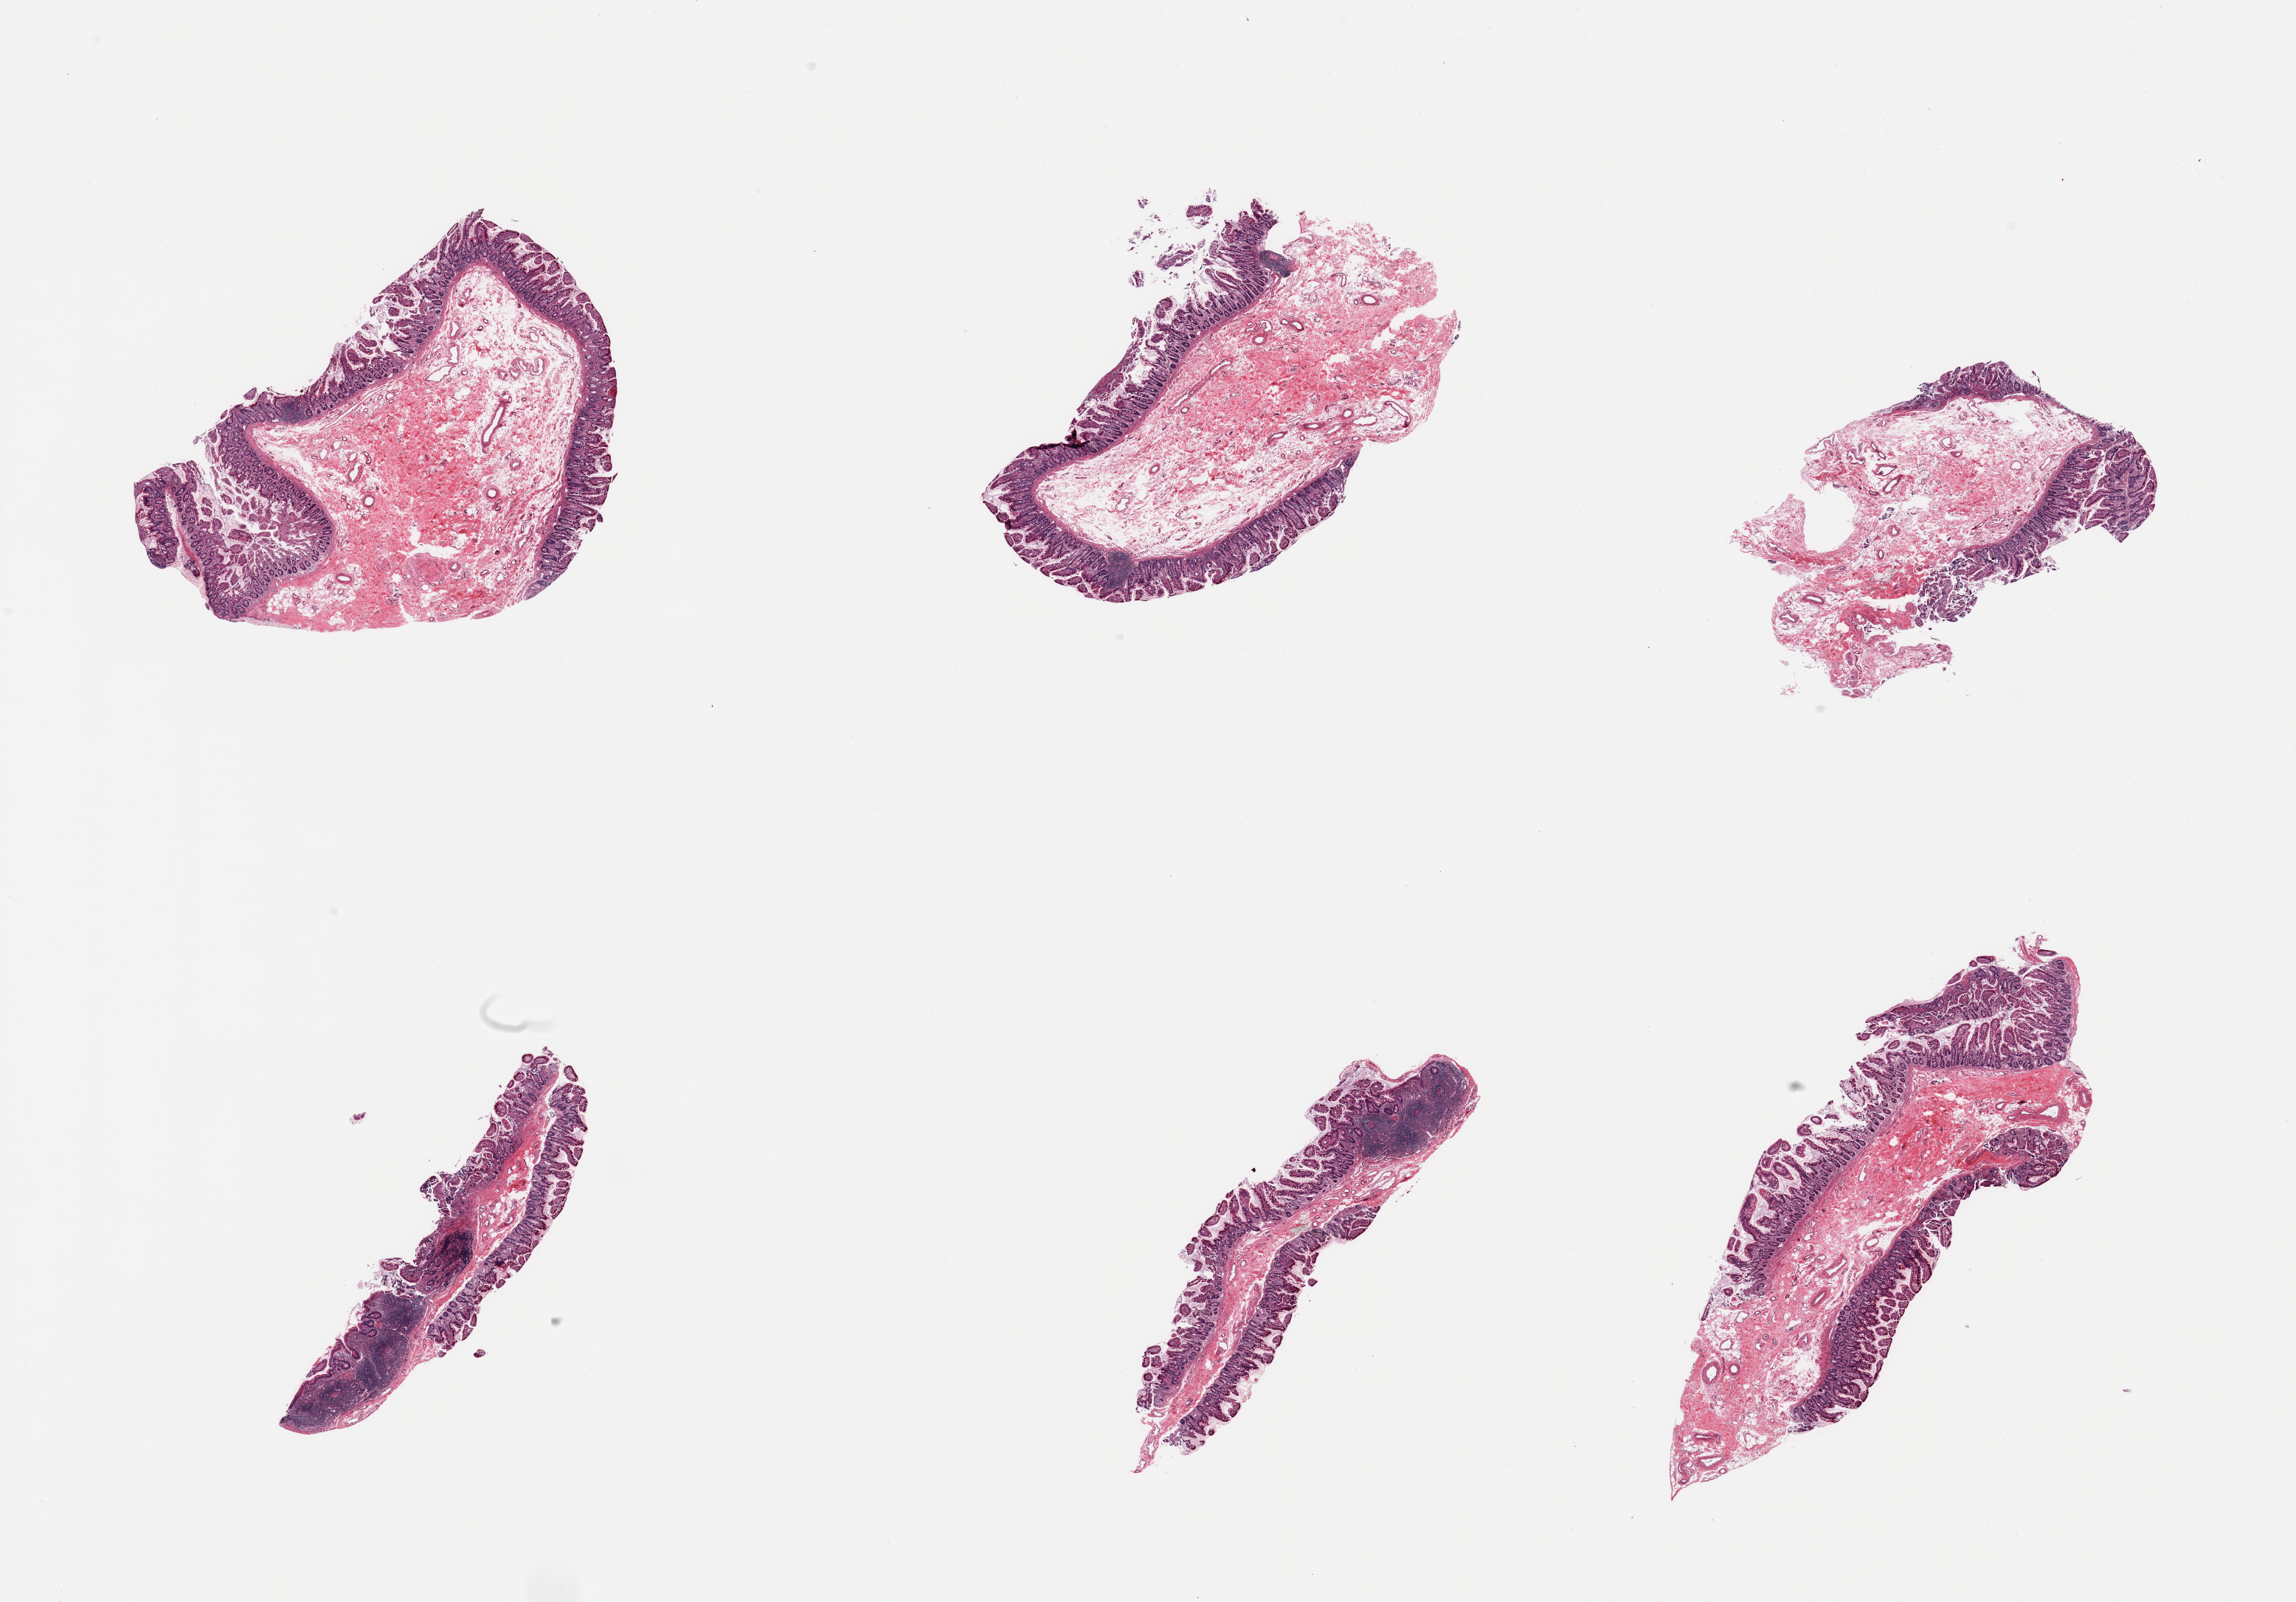
Digitized haematoxylin and eosin-stained section, a low-resolution overview of the entire scanned area, about 24.6 x 17.2 mm. PAXgene-fixed, paraffin-embedded tissue. Section of ileum (target tissue). Tissue donor sample.
Review note (as recorded): 6 pieces, ~10-15% well -preserved target lymphoid aggregates.